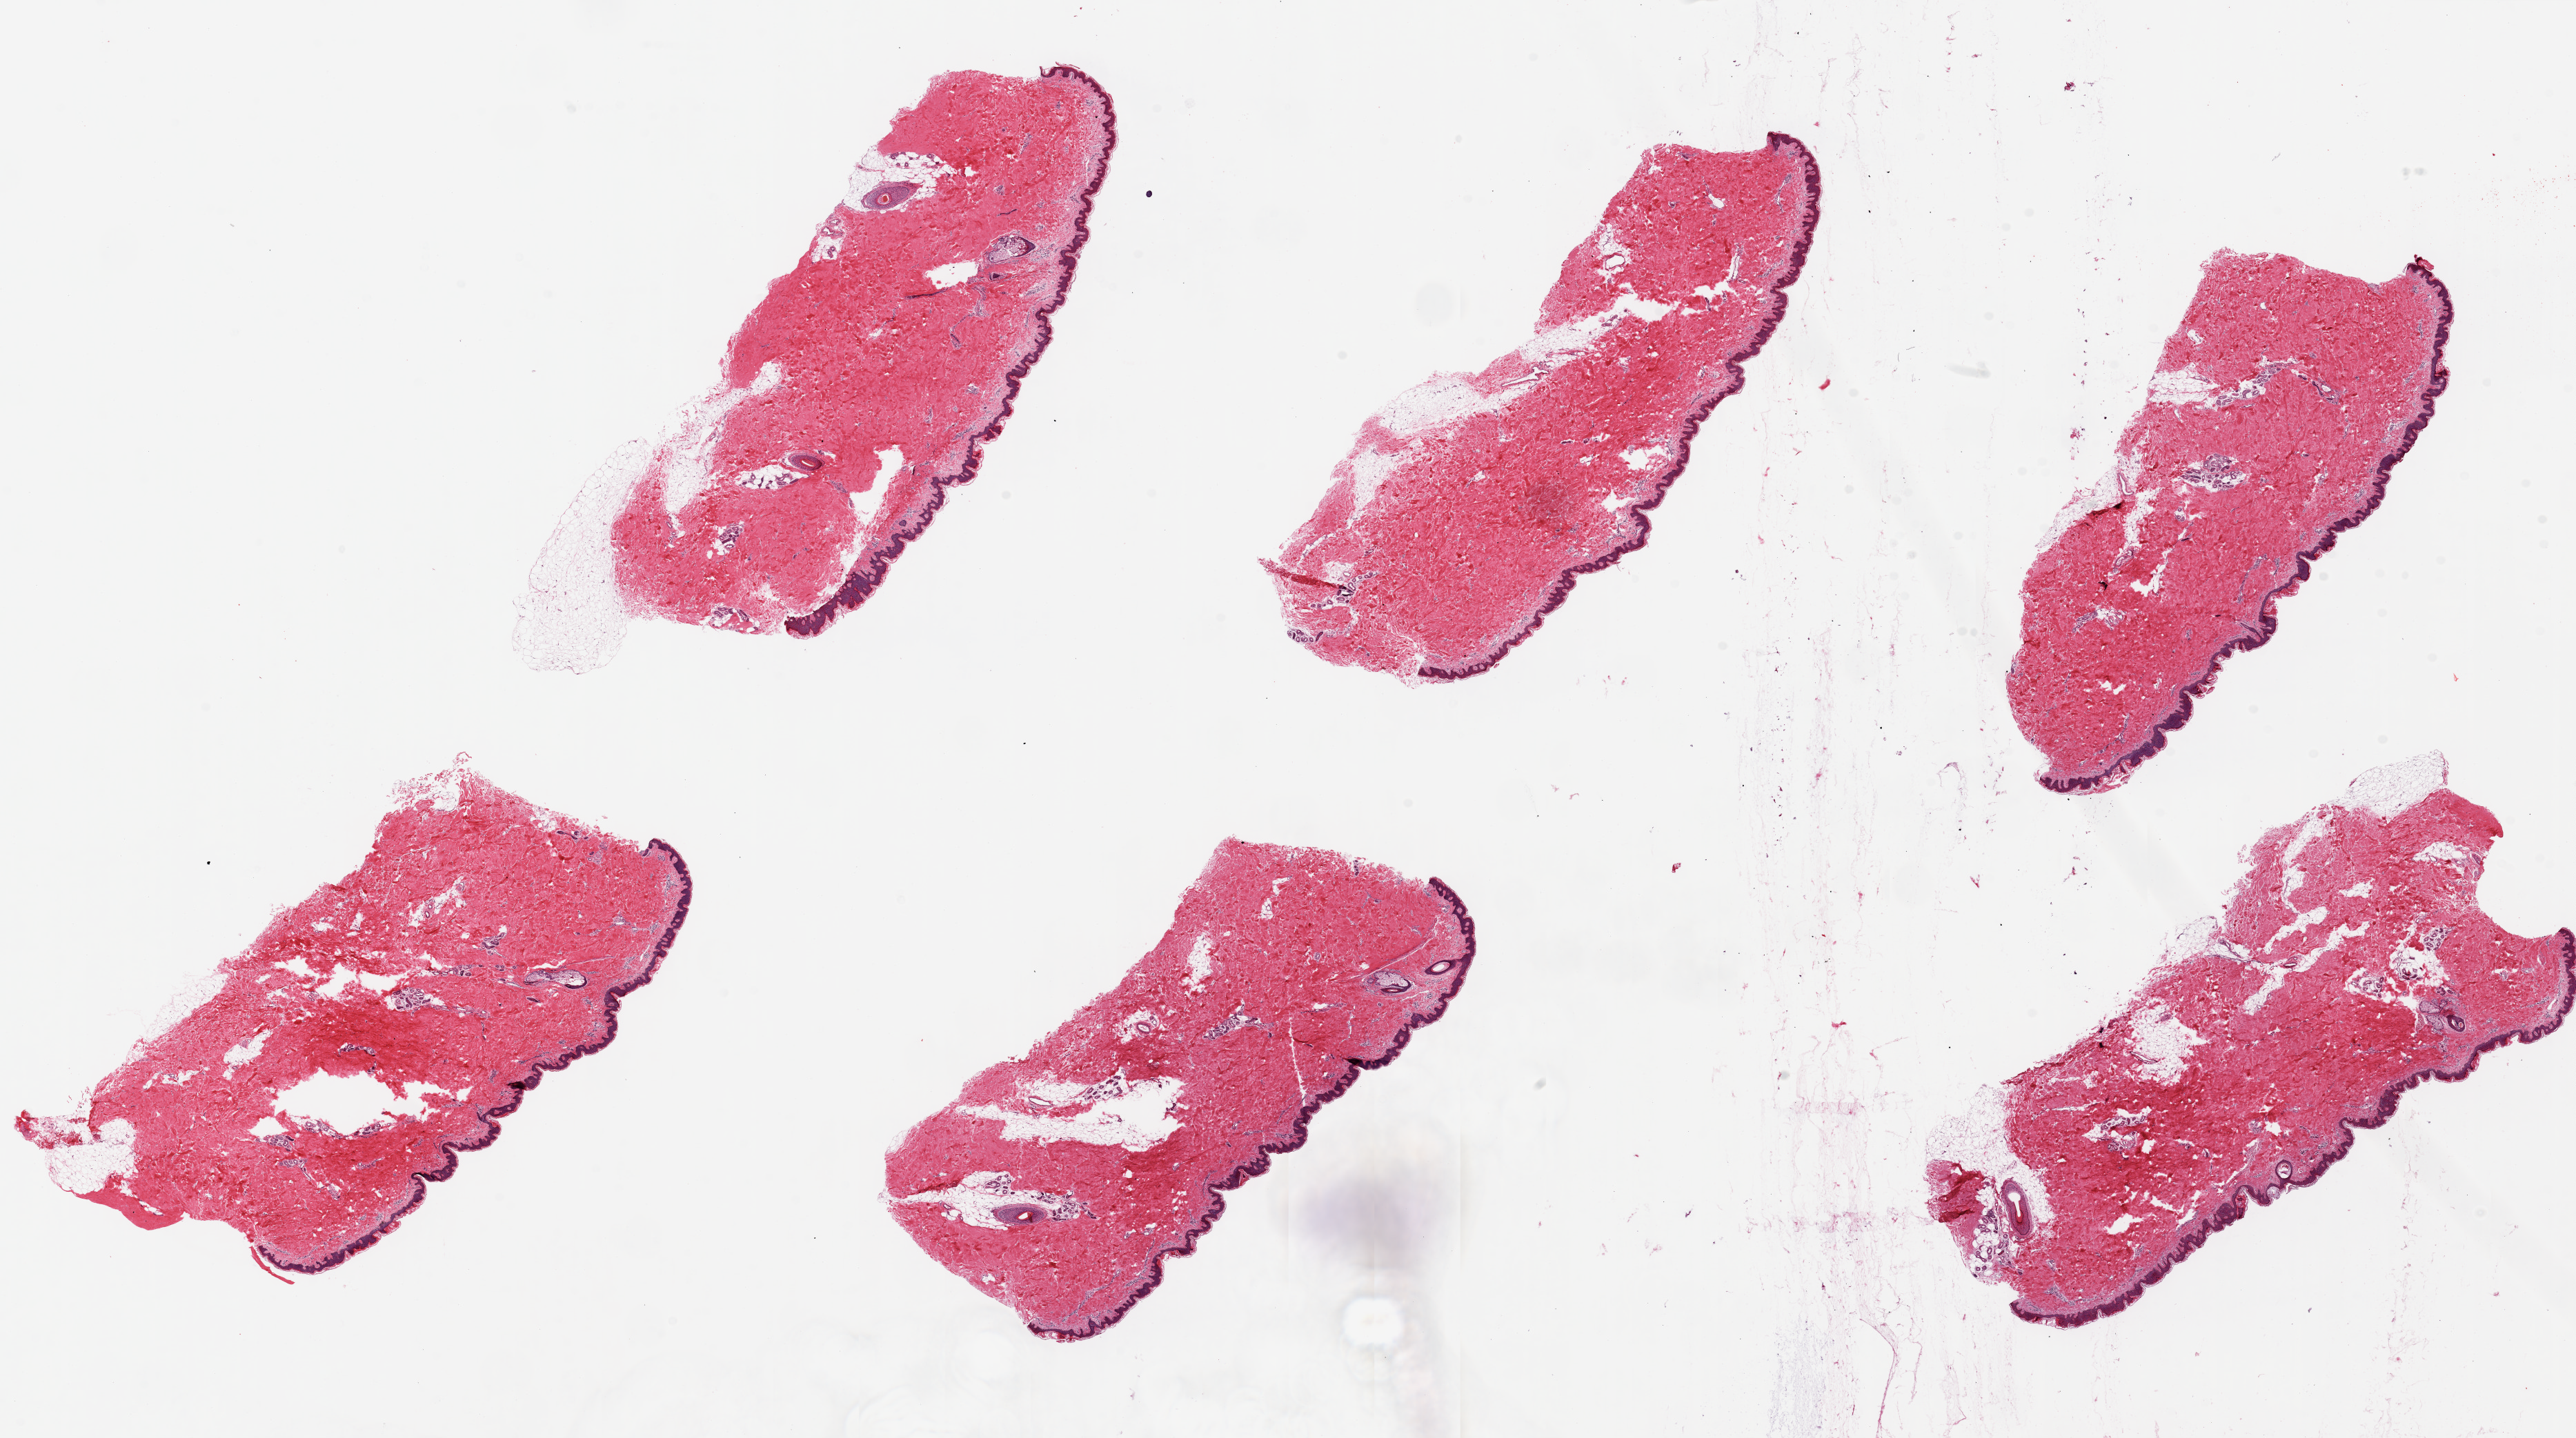
H&E whole-slide image — a low-resolution overview of the entire scanned area, about 29.5 x 16.5 mm (acquisition: 20x scan). PAXgene-fixed paraffin-embedded (PFPE) section. Target tissue: skin of lower leg. Tissue donor sample. Male donor.
* review note (as recorded): 6 pieces ~7x2.5mm Squamous epithelium is ~2% thickness